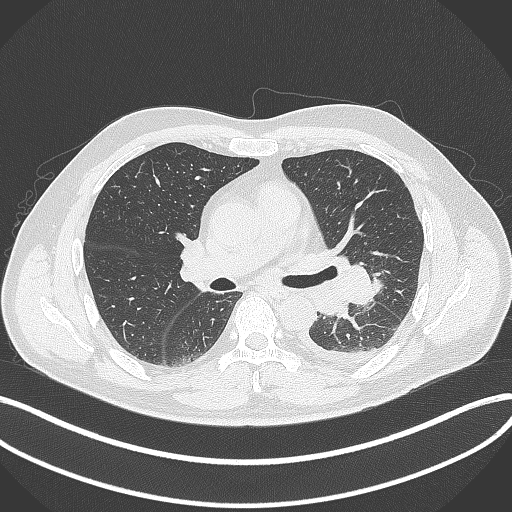
Chest CT, one axial slice. Slice 208 of 342 in the series (ordered by position). Reconstruction kernel B70f. 120 kVp. Lung window (W 1500 / L -600 HU). 512 × 512 image matrix, field of view 400 × 400 mm. Male patient, age 58 years. From the clinical record (not read from this slice): clinical TNM (as recorded): T3 N1 M1b.
Outlined on this slice (rectangle marked by the reading radiologist):
- lung tumour (recorded histology: small cell carcinoma): bounding box <344,258,377,307> (left, top, right, bottom; pixels)